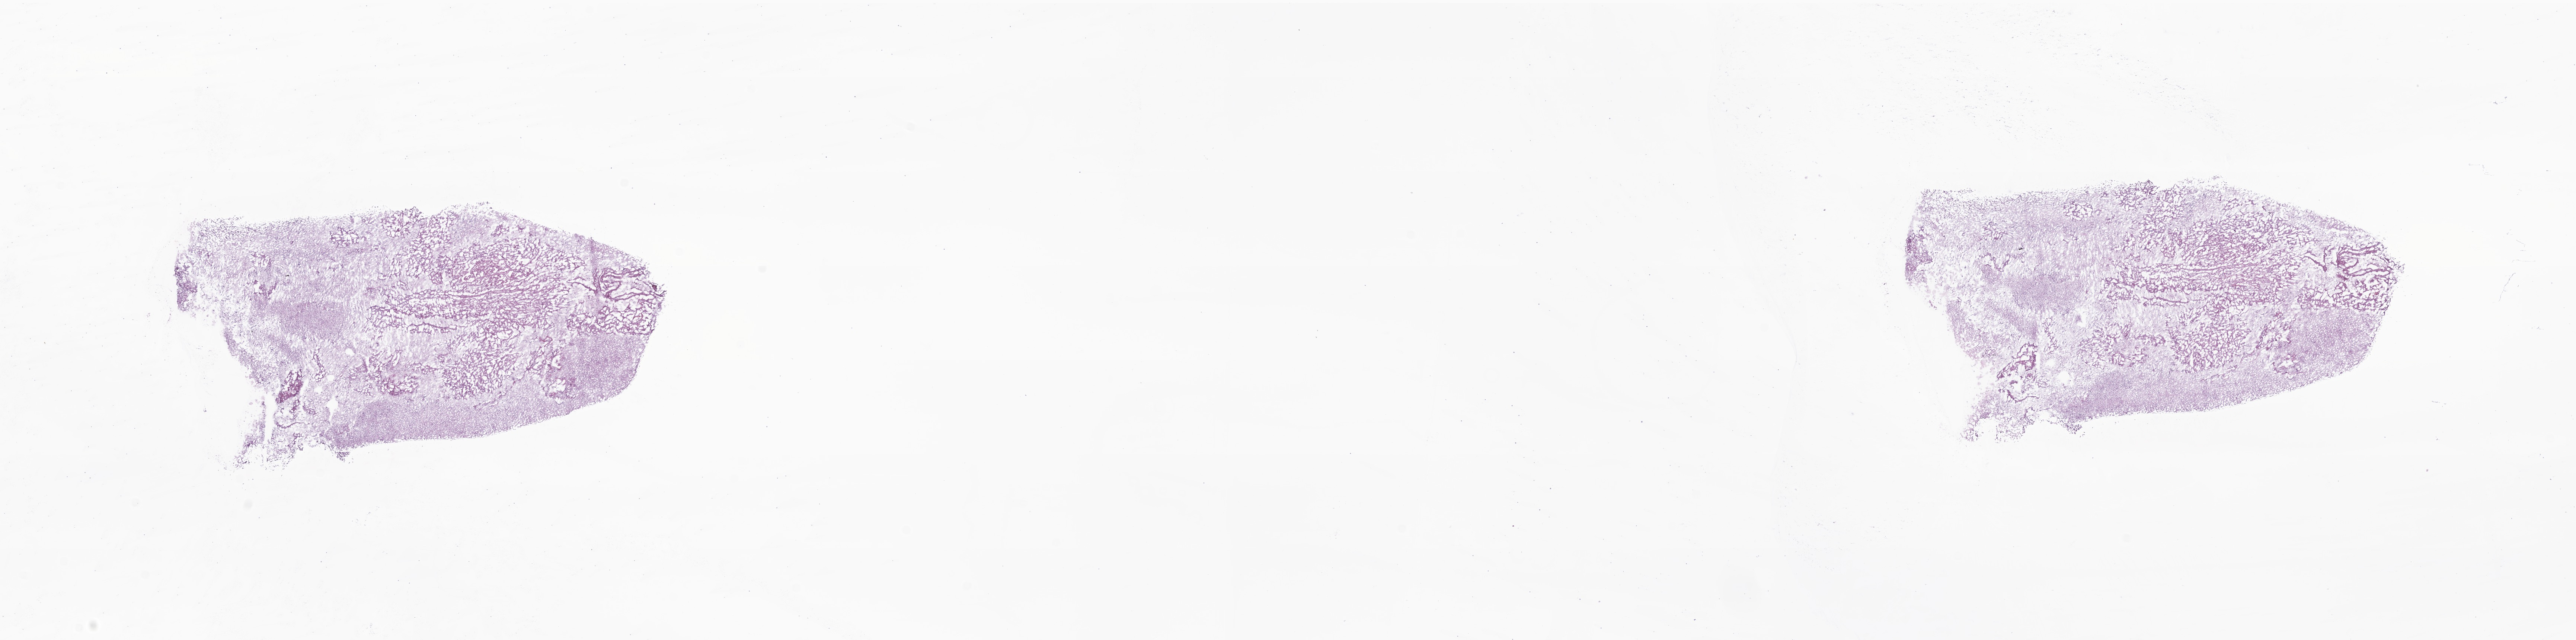
Digitized H&E-stained section of tumor tissue from the cerebellum — shown as a low-resolution overview of the whole scanned area (about 29.2 x 7.3 mm), frozen section. Male patient, age 120 months (10 years).
• diagnosis (ICD-O-3 morphology term): Astrocytoma, NOS